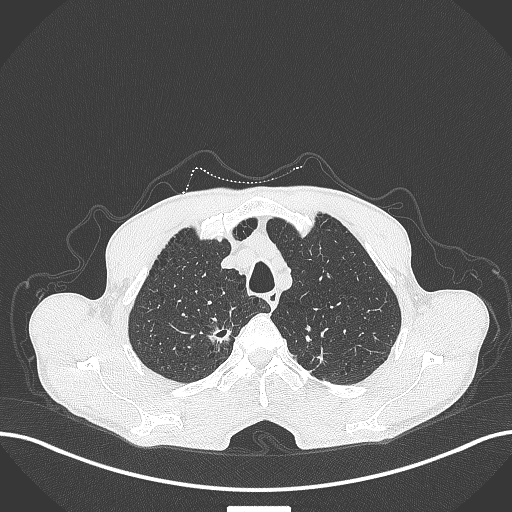
Chest CT, one axial slice. Slice 357 of 445 in the series (ordered by position). 120 kVp. Lung window (W 1500 / L -600 HU). 1 mm slice thickness. 512 × 512 image matrix, field of view 400 × 400 mm. Male patient, age 70 years. Case-level facts recorded for this patient, not image findings: clinical TNM (as recorded): T1a N0 M0.
Outlined on this slice (rectangle marked by the reading radiologist):
- lung tumour (recorded histology: adenocarcinoma): bounding box (x1, y1, x2, y2) in pixels: (208, 323, 234, 348)